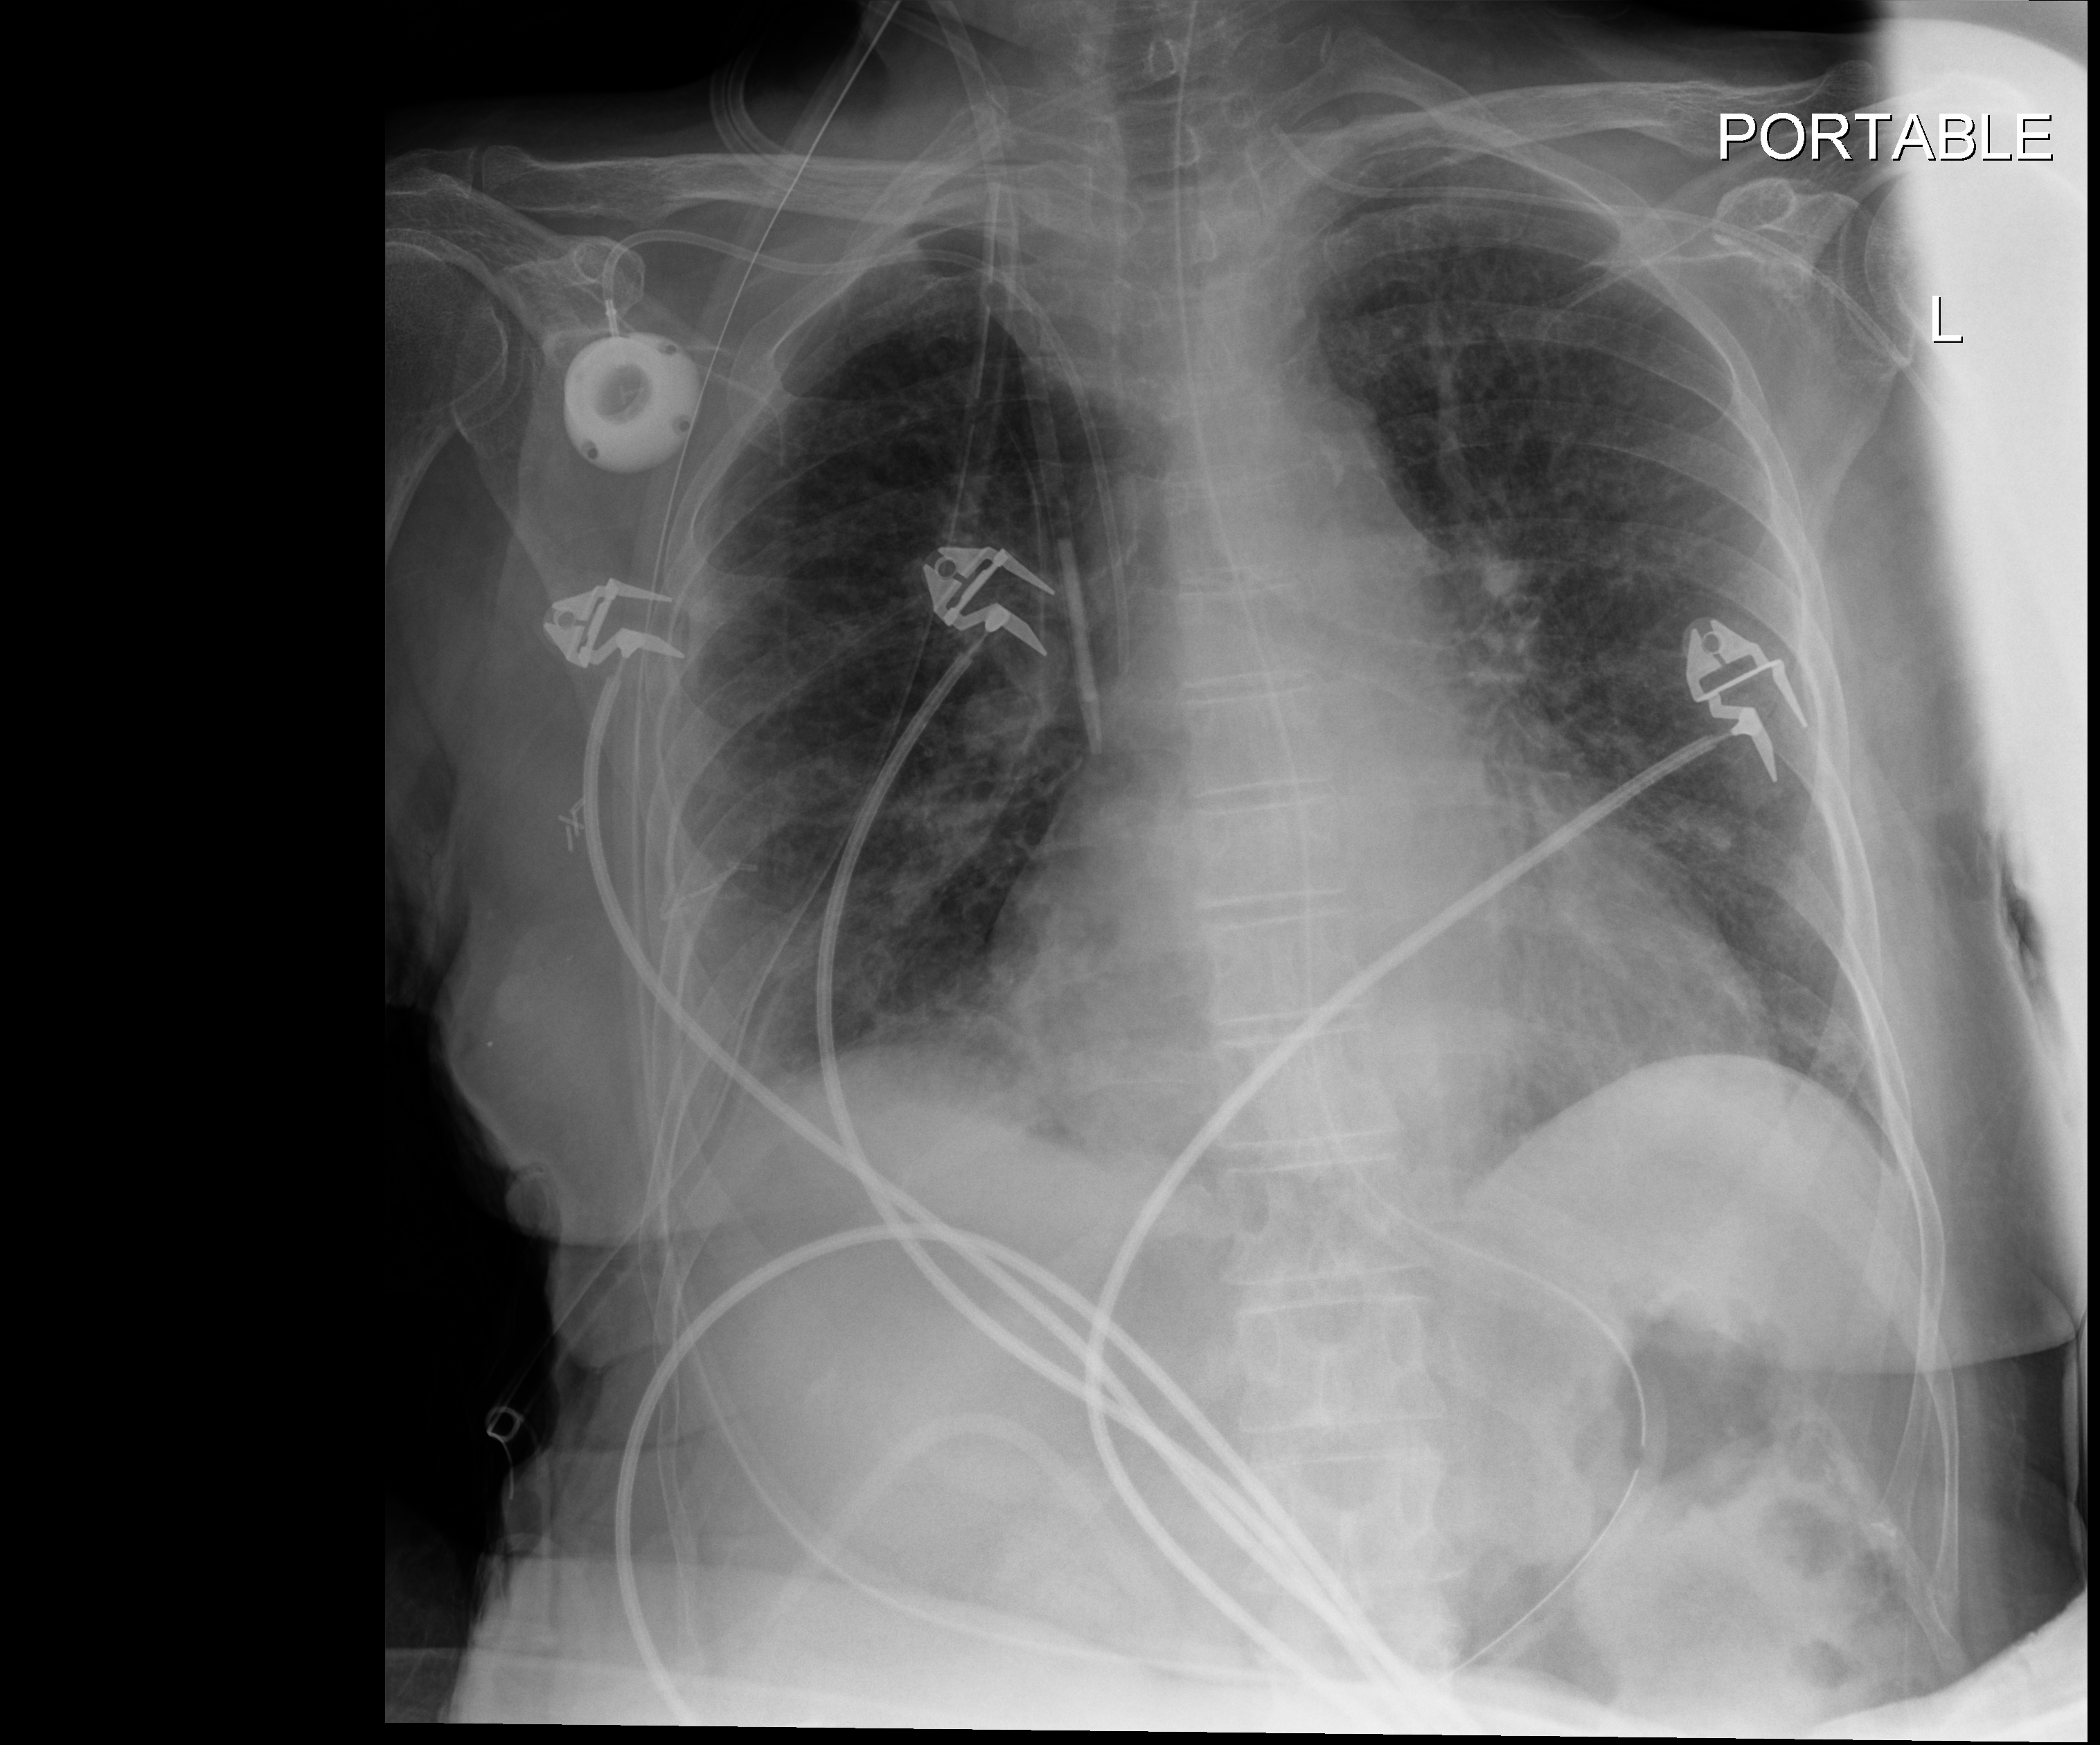
Bedside chest radiograph (digital radiography), anteroposterior (AP) projection. Patient hospitalised with COVID-19; female, aged 60–74 years.
Hospital-stay facts (about this admission, not read from this image; timing relative to this image not recorded): COPD (admission record): no; length of hospital stay: 43 days; admitted to intensive care during this hospital stay: yes.